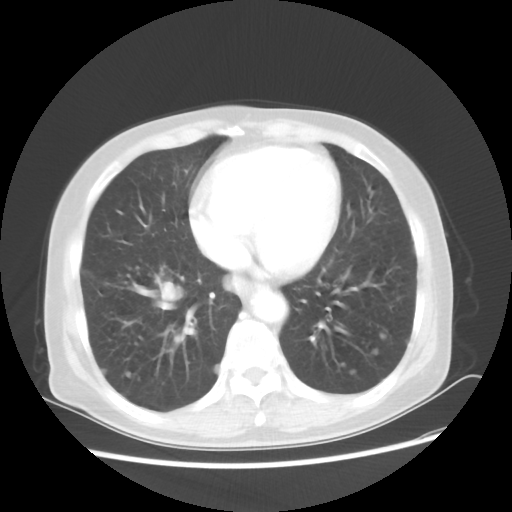
Chest CT, one axial slice. Position 19 of 56 along the scan axis. Reconstruction kernel STANDARD. 80 kVp. Lung window (W 1500 / L -600 HU). 5 mm slice thickness. 512 × 512 image matrix, field of view 360 × 360 mm. Patient: female, 68 years. From the clinical record (not read from this slice): clinical TNM (as recorded): T1c N3 M0.
Outlined on this slice (bounding box drawn by a radiologist):
- lung tumour (recorded histology: squamous cell carcinoma): bounding box [x1, y1, x2, y2] px = [145, 268, 195, 327]